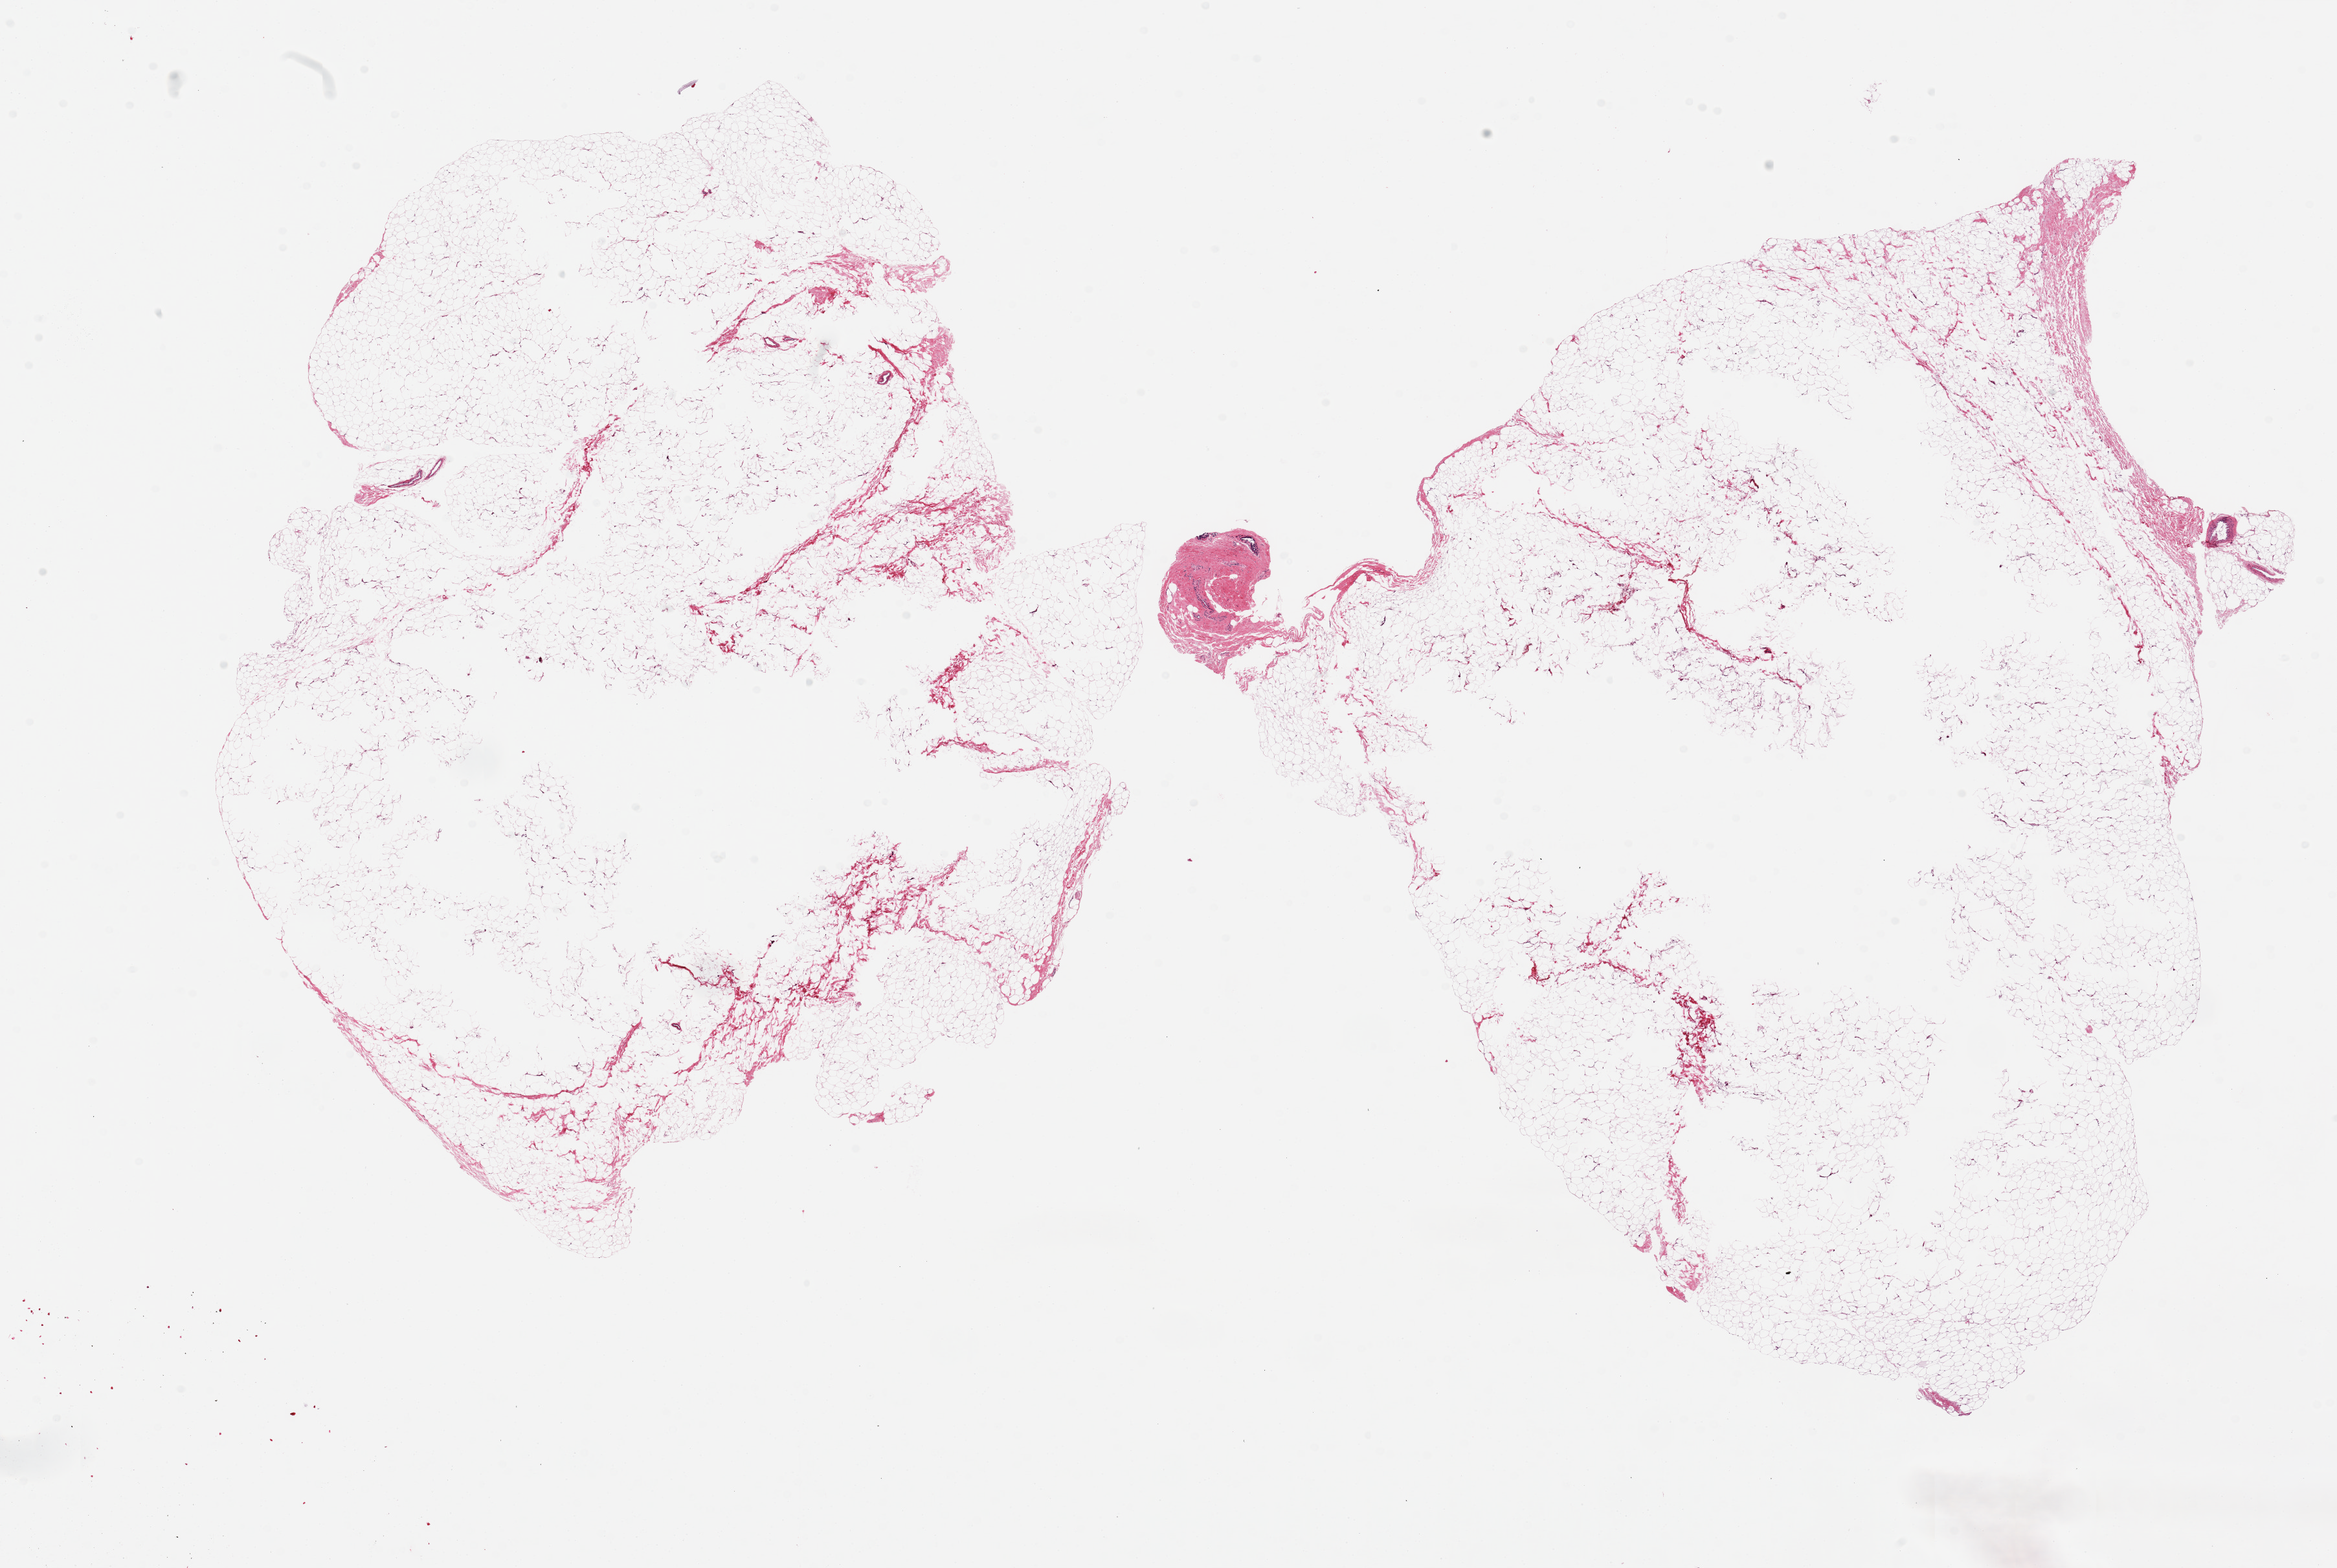
Whole-slide image, haematoxylin and eosin stain — a low-resolution overview of the entire scanned area, about 28.5 x 19.2 mm (slide scanned at 20x), PAXgene-fixed paraffin-embedded (PFPE) section, sampled site (target tissue): breast, tissue donor sample.
Pathologist's review note for this sample: 2 pieces ~14x10mm, all fat, no ductal elements seen.